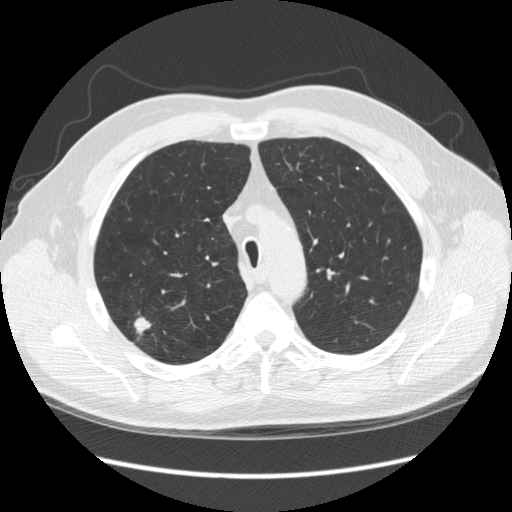
Axial slice from a low-dose chest CT screening exam; third annual screen; lung window (W 1500 / L -600 HU); standard (soft-tissue) reconstruction kernel (STANDARD); slice 61 of 248 in the series. Male participant, aged 64 years at enrolment. Former smoker at enrolment.
Expert-annotated lung lesion, bounding box [x1, y1, x2, y2] px = [118, 313, 169, 355]. The screening reader recorded 4 non-calcified nodules or masses ≥4 mm on this exam; which of them this box marks is not recorded. Participant outcome: lung cancer diagnosed 15 days after this screen — adenocarcinoma, NOS, right upper lobe, moderately differentiated (G2), stage IA (AJCC 6th edition), 14 mm at pathology.